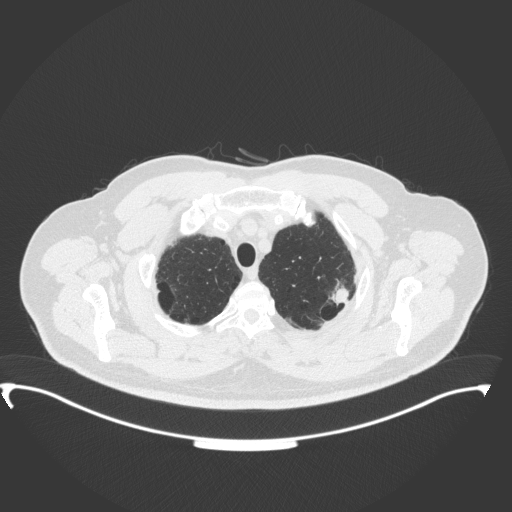
Chest CT, one axial slice. Position 317 of 350 along the scan axis. Lung window (W 1500 / L -600 HU). 1 mm slice thickness. 512 × 512 image matrix, field of view 459 × 459 mm. Male patient, age 64 years. From the clinical record (not read from this slice): clinical TNM (as recorded): T1c N1 M1.
Outlined on this slice (bounding box drawn by a radiologist):
- lung tumour (recorded histology: adenocarcinoma): box from (x=327, y=282) to (x=351, y=306) px